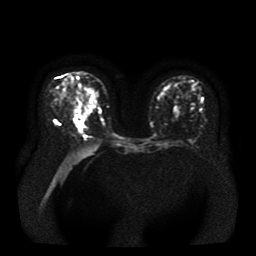
Breast MRI, one axial slice; slice 17 of 41 in the series (ordered by position); diffusion-weighted series; image 2 of 4 stored at this slice position (different b-values; order by instance number); 1.5 T; 5 mm slice thickness; 256 × 256 image matrix, field of view 330 × 330 mm. Female patient.
Structures marked on this image (outlined manually by an expert reader):
- tumour on diffusion-weighted imaging: bounding box <75,110,84,125> (left, top, right, bottom; pixels)